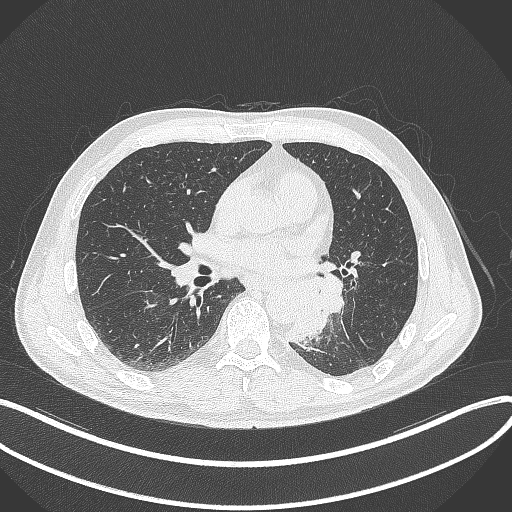
Chest CT, one axial slice. Slice 163 of 329 in the series (ordered by position). Reconstruction kernel B70f. Lung window (W 1500 / L -600 HU). 1 mm slice thickness. 512 × 512 image matrix, field of view 400 × 400 mm. Patient: male, 59 years. Case-level facts recorded for this patient, not image findings: clinical TNM (as recorded): T2a N2 M0.
Outlined on this slice (bounding box drawn by a radiologist):
- lung tumour (recorded histology: squamous cell carcinoma): bounding box <292,270,344,348> (left, top, right, bottom; pixels)